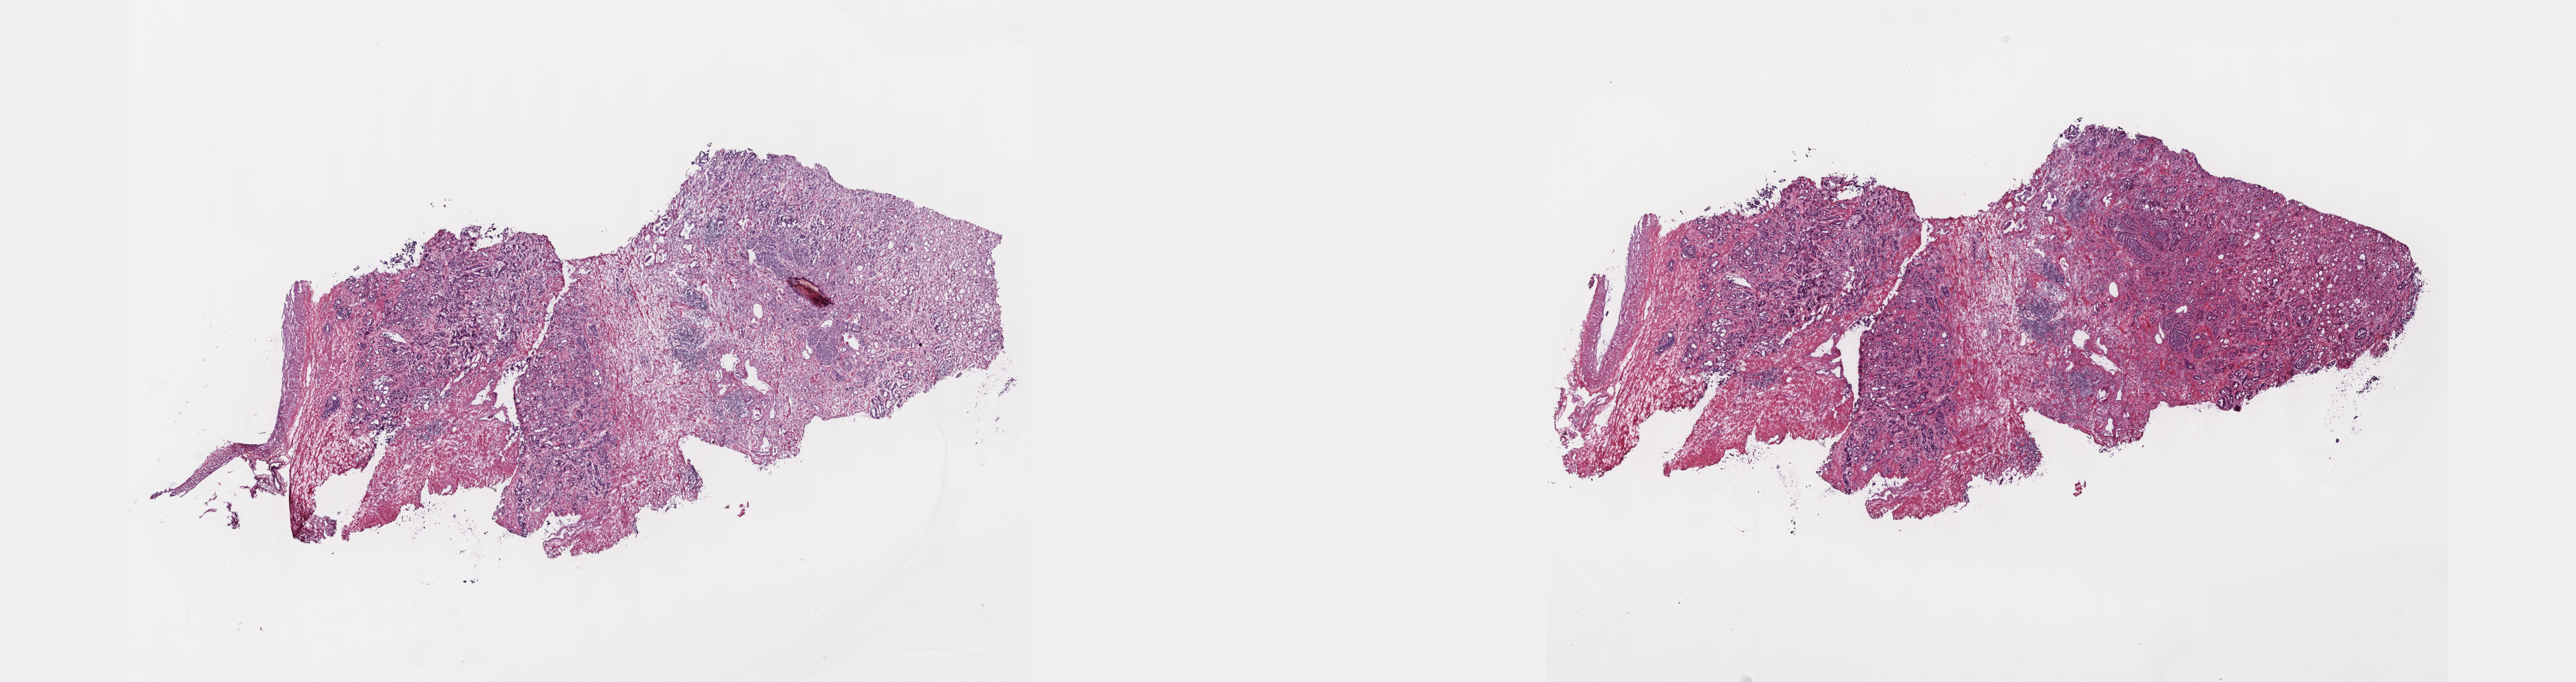
Whole-slide histology image, H&E-stained — low-resolution overview of the scanned area, about 30.2 x 8.0 mm (slide scanned at 40x). Frozen section from the top of the tissue portion. Prostate, primary tumour sample. Male, age 64 years at initial diagnosis. Gleason score: 7 (4+3). Slide review estimates, as recorded: tumour cells 55%, tumour nuclei 70%, normal cells 5%, stromal cells 40%, necrosis 0%. Infiltration values recorded for this section: lymphocyte infiltration 0%, monocyte infiltration 0%, neutrophil infiltration 0%.
Pathologic diagnosis: Adenocarcinoma, NOS. Lymph nodes positive (case pathology): 0 of 11 examined. Laterality: left.